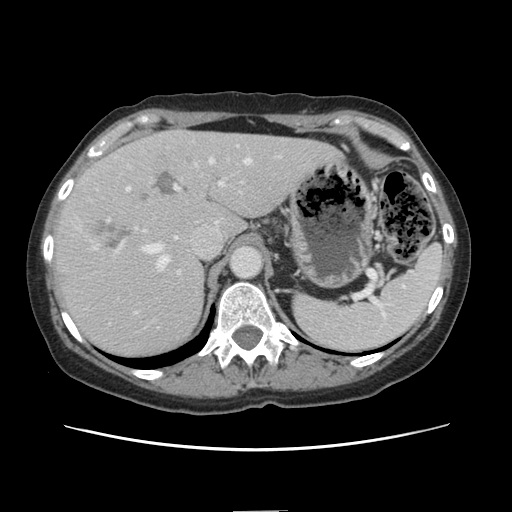
Contrast-enhanced abdominal CT, one axial slice; position 102 of 141 along the scan axis; intravenous contrast given; soft-tissue window (W 400 / L 40 HU); 2.5 mm slice thickness; 512 × 512 image matrix, field of view 350 × 350 mm. Female patient, age 63 years. Case-level facts recorded for this patient, not image findings: diagnosis: colorectal cancer liver metastases, imaged before liver resection; multiple liver metastases: yes; largest metastasis: 3.2 cm; disease in both lobes: yes.
Annotated regions visible in this slice (manually delineated by an expert):
- hepatic veins: box from (x=143, y=159) to (x=250, y=267) px
- liver: (x=53, y=131)–(x=336, y=358)
- planned liver remnant (the part of the liver to remain after resection): (x=186, y=132)–(x=337, y=238)
- portal vein (with intrahepatic branches): (x=126, y=181)–(x=225, y=274)